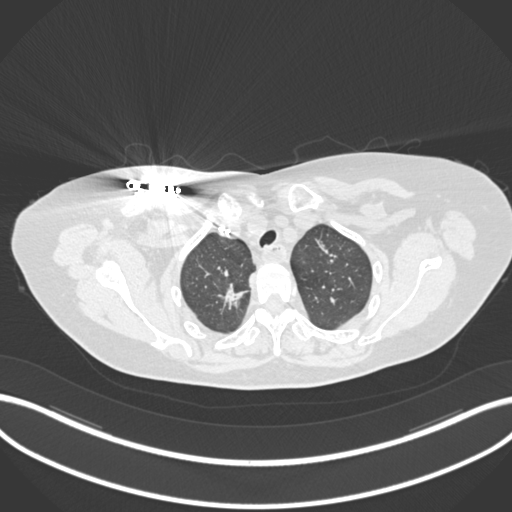
Chest CT, one axial slice; slice 151 of 176 in the series (ordered by position); 120 kVp; lung window (W 1500 / L -600 HU); 1 mm slice thickness; 512 × 512 image matrix. Female patient, age 72 years. From the clinical record (not read from this slice): clinical TNM (as recorded): T1c N0 M0.
Structures marked on this image (rectangle marked by the reading radiologist):
- lung tumour (recorded histology: adenocarcinoma): bounding box (x1, y1, x2, y2) in pixels: (212, 283, 248, 308)